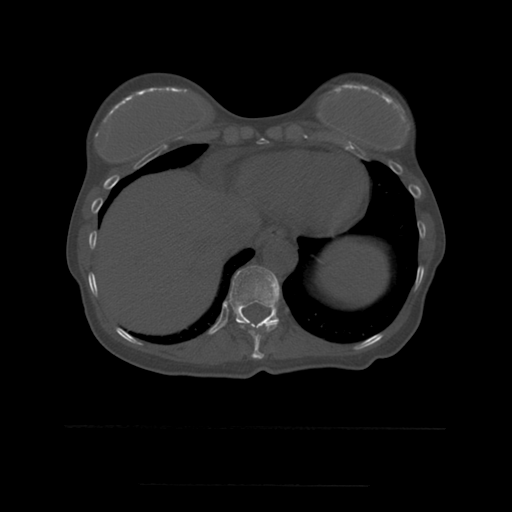
CT including the spine, one axial slice; position 290 of 544 along the scan axis; bone window (W 1800 / L 400 HU); 1.25 mm slice thickness; 512 × 512 image matrix, field of view 350 × 350 mm. Patient age 58 years. Case-level facts recorded for this patient, not image findings: primary cancer: lung.
Outlined on this slice (semi-automatically segmented with operator editing):
- T10 vertebra: bounding box (x1, y1, x2, y2) in pixels: (239, 322, 279, 359)
- T11 vertebra: (219, 266, 280, 324)